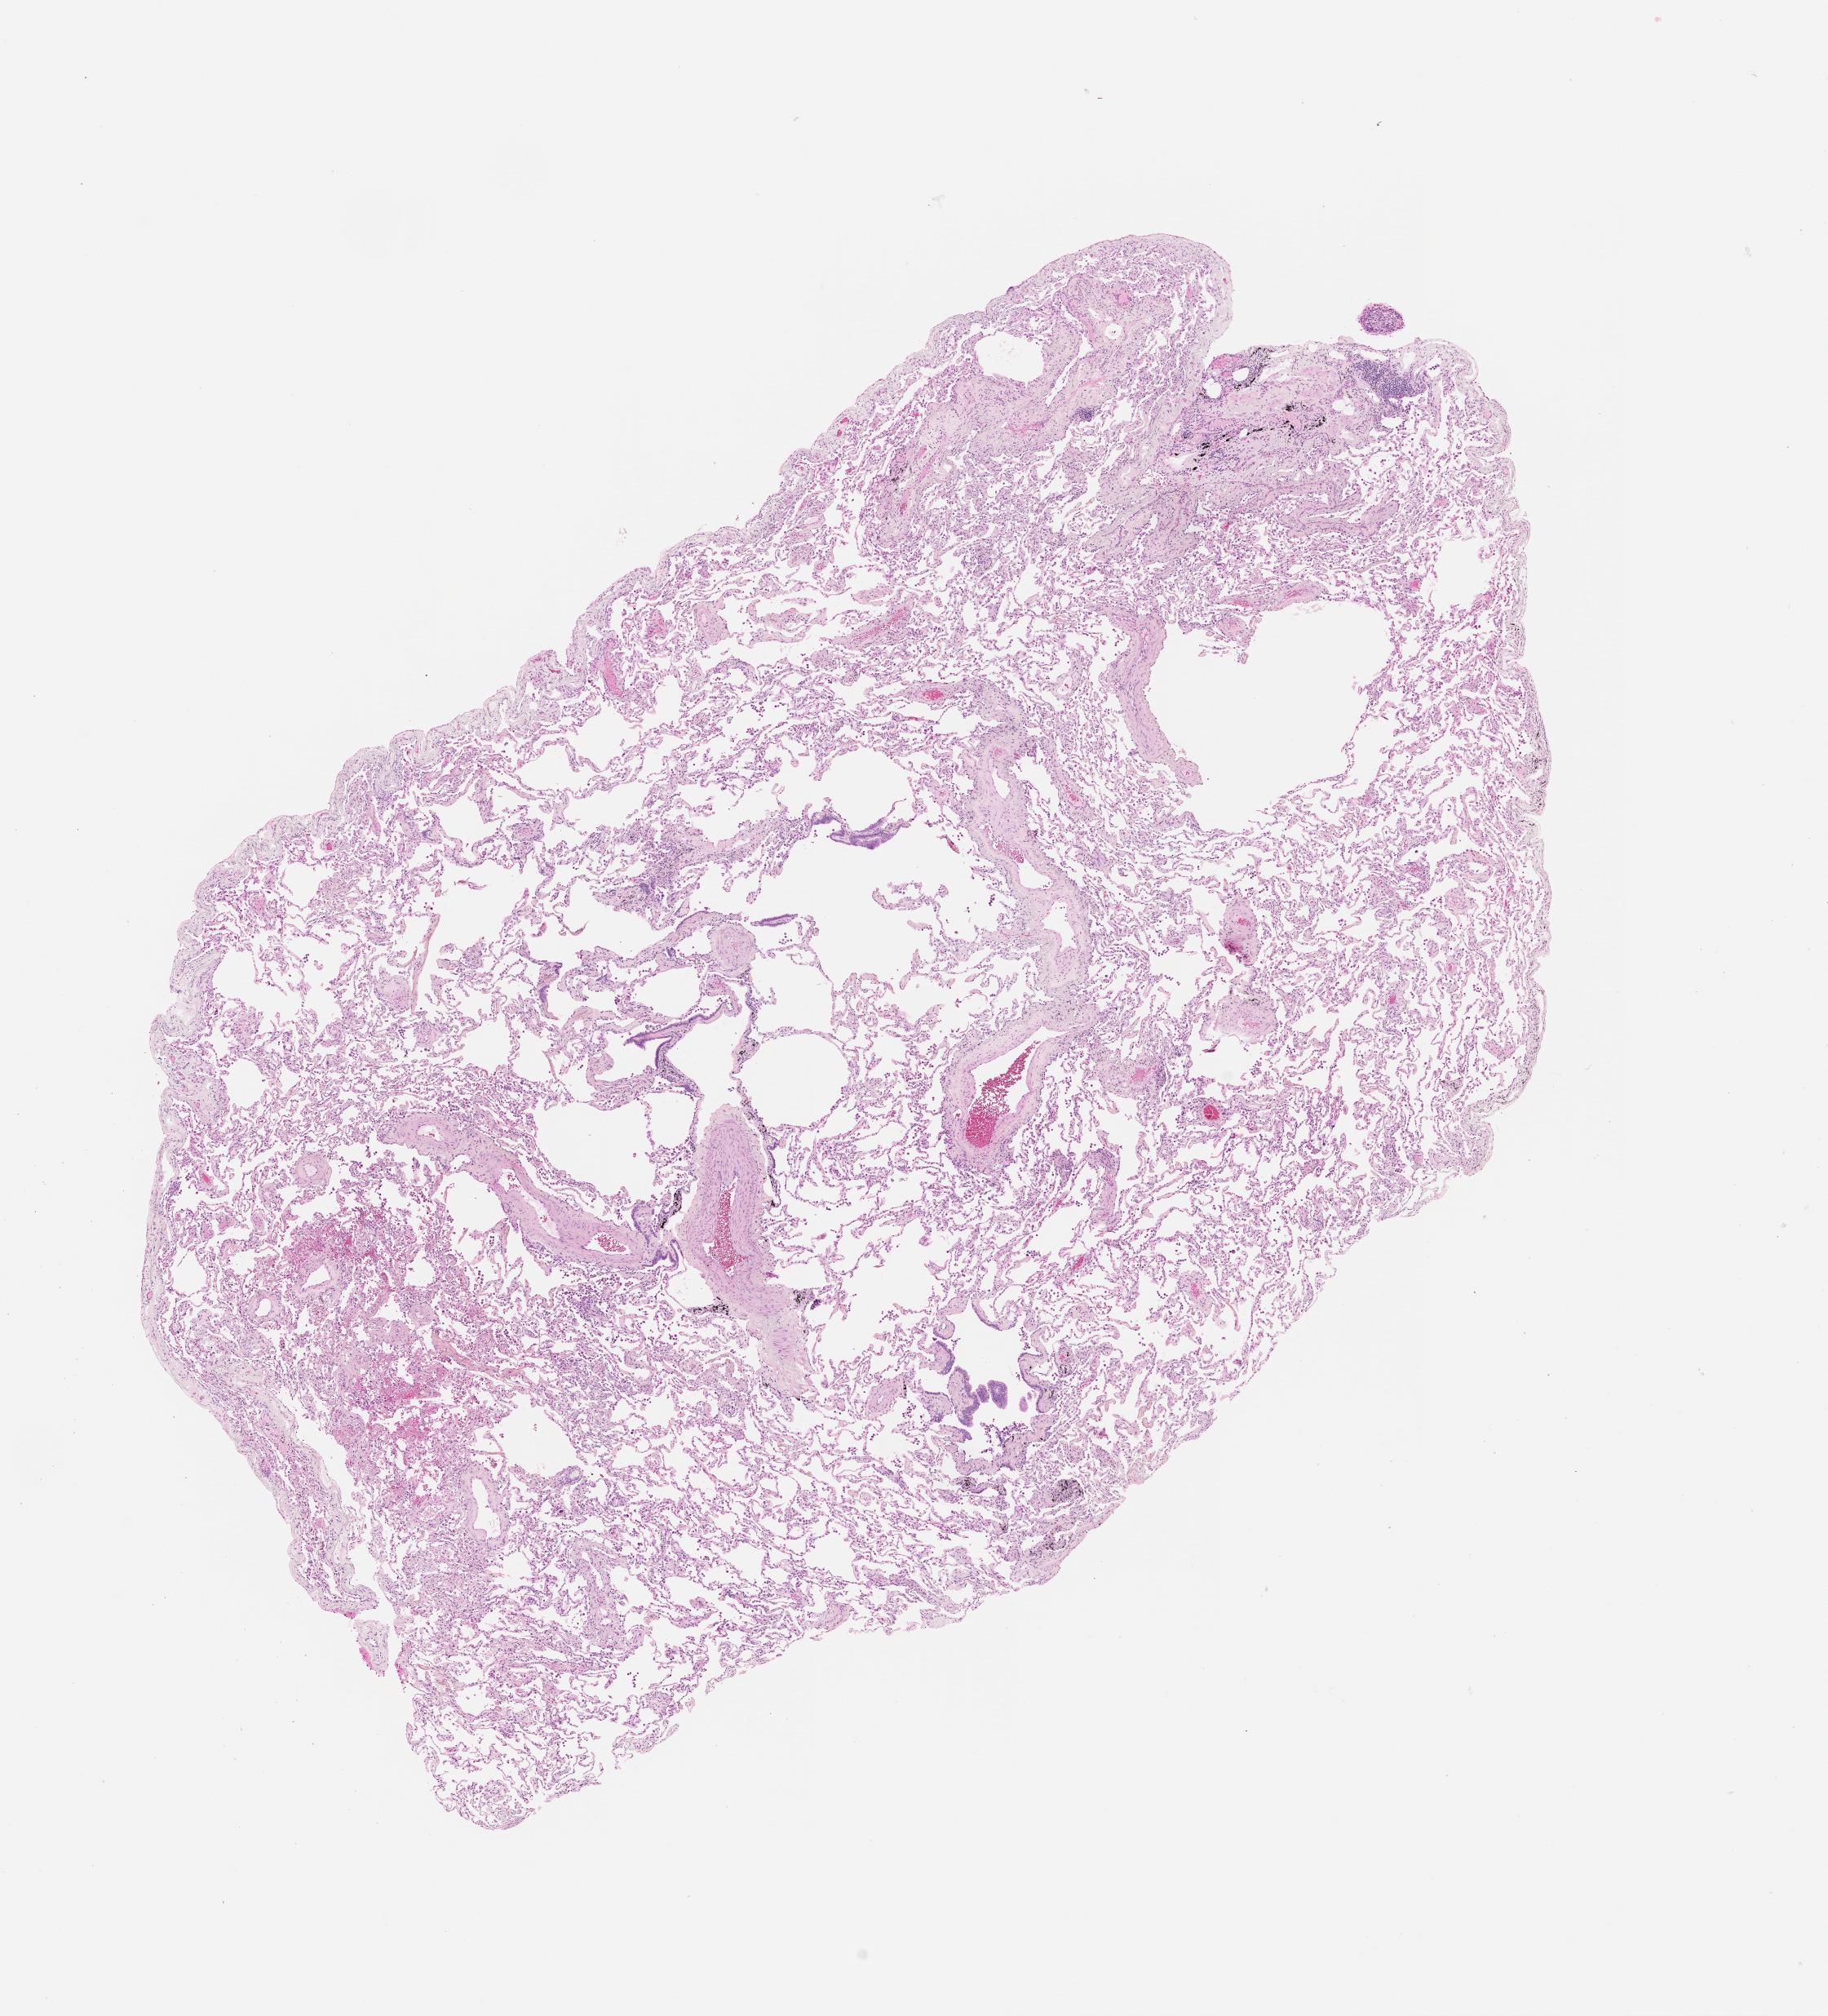
H&E whole-slide image — a low-resolution overview of the entire scanned area, about 9.0 x 9.9 mm (acquisition: 20x scan); lung, normal (non-tumour) tissue. Patient: male, age 69 years.
This section: normal (non-tumour) tissue from the same patient. Patient diagnosis (cohort enrolment): squamous cell carcinoma (lung).